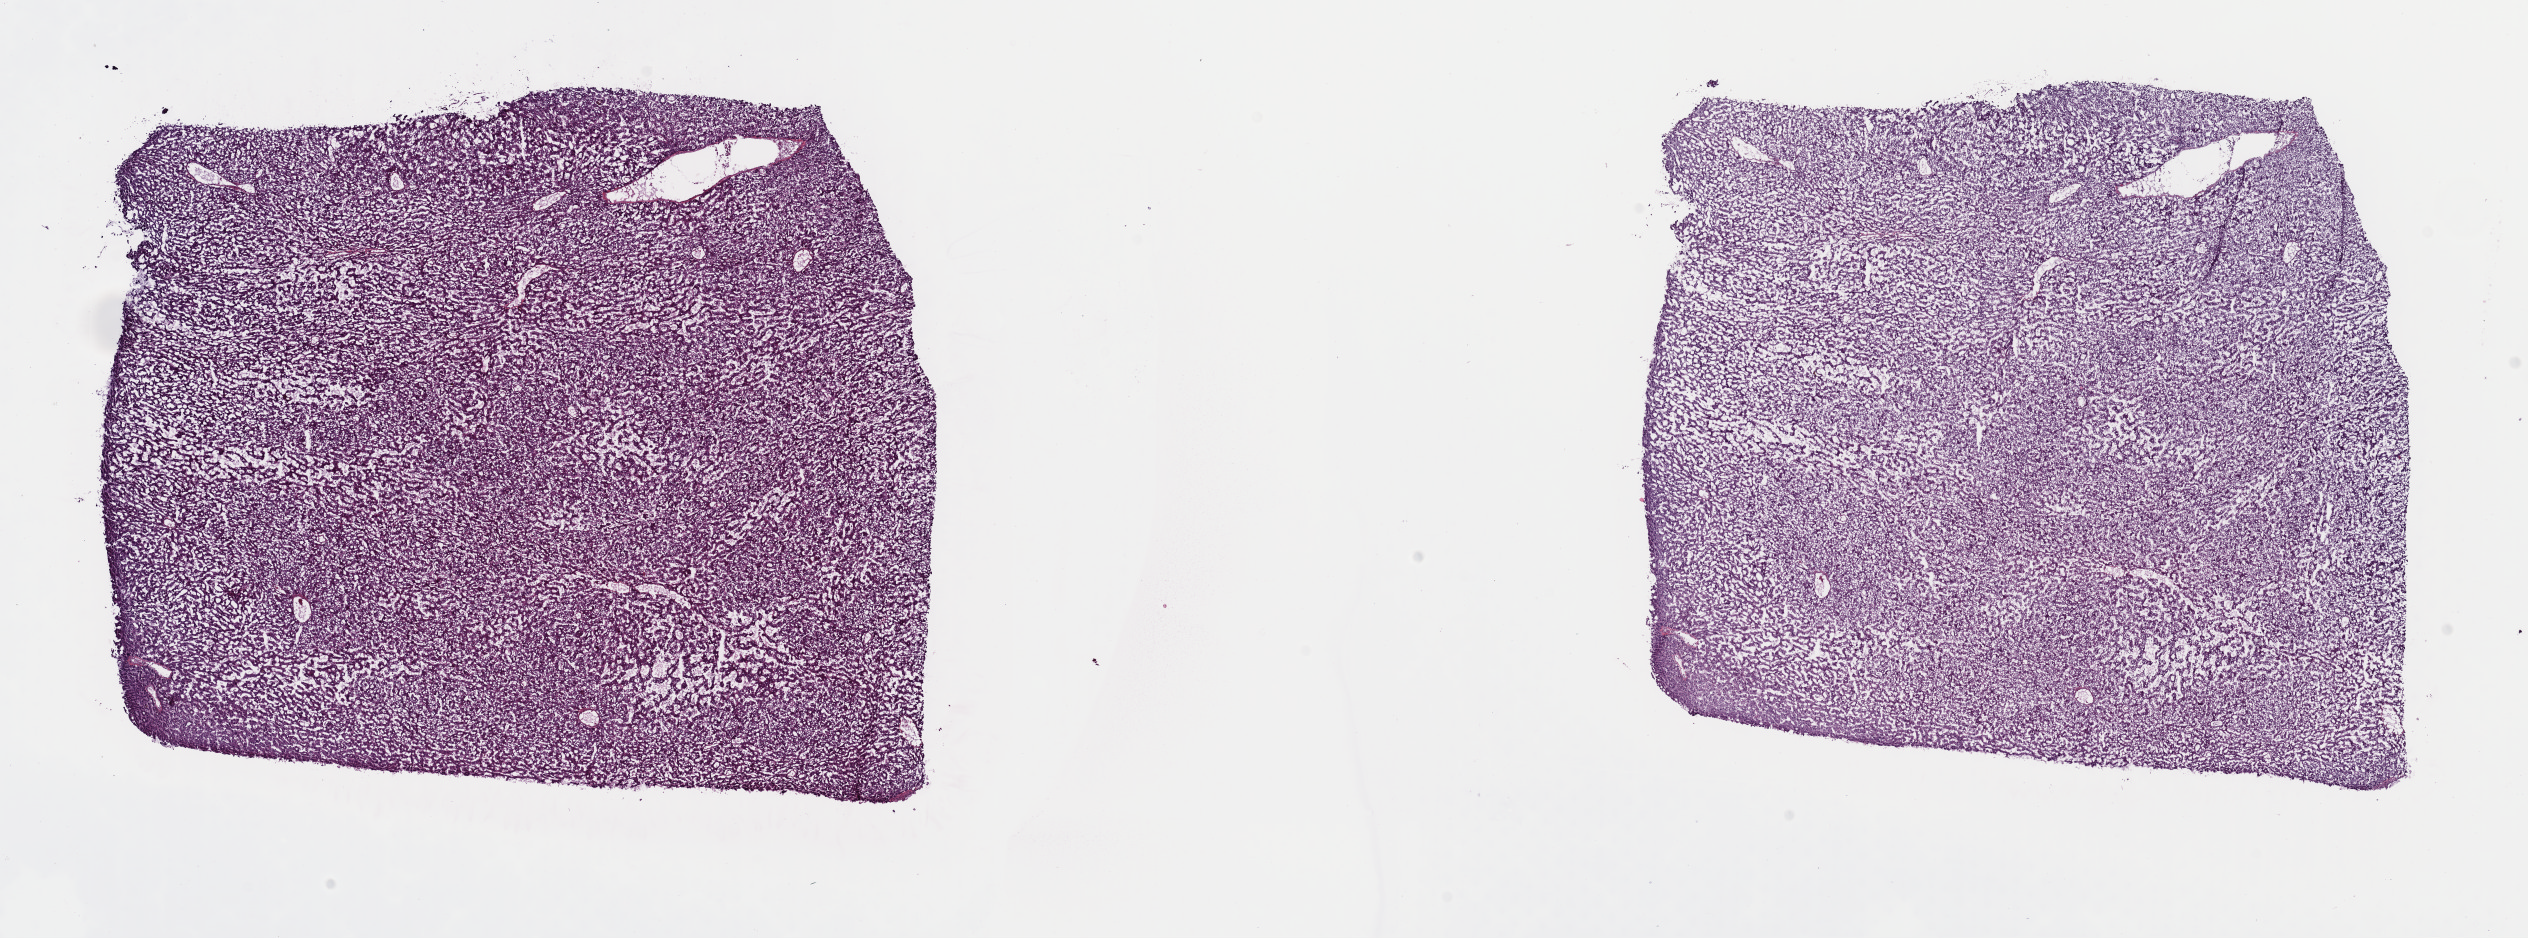
Whole-slide histology image, Hematoxylin and eosin (H&E) stained — a low-resolution overview of the entire scanned area, about 20.0 x 7.4 mm (acquisition: 40x scan). Frozen section. Liver, primary tumour sample. Patient: male, age at initial diagnosis 32 years.
Pathologic diagnosis: Hepatocellular carcinoma, NOS.